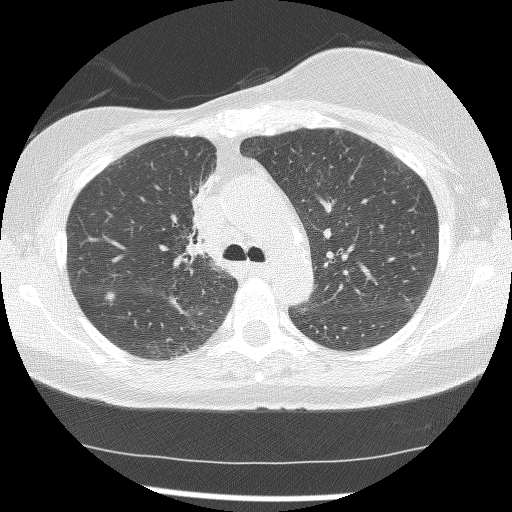
Chest CT (low-dose screening protocol), one axial image, baseline annual screen, lung window (W 1500 / L -600 HU), 2.5 mm slice thickness, 512 × 512 image matrix. Female participant, aged 56 years at enrolment.
Lesion marked by an expert reader, box from (x=163, y=169) to (x=219, y=265) px. The screening reader recorded 2 non-calcified nodules or masses ≥4 mm on this exam (right lower lobe, right middle lobe); which of them this box marks is not recorded. Participant outcome: lung cancer diagnosed 1185 days after this screen — adenocarcinoma, NOS, right upper lobe, stage IIIB (AJCC 6th edition), 8 mm at pathology.